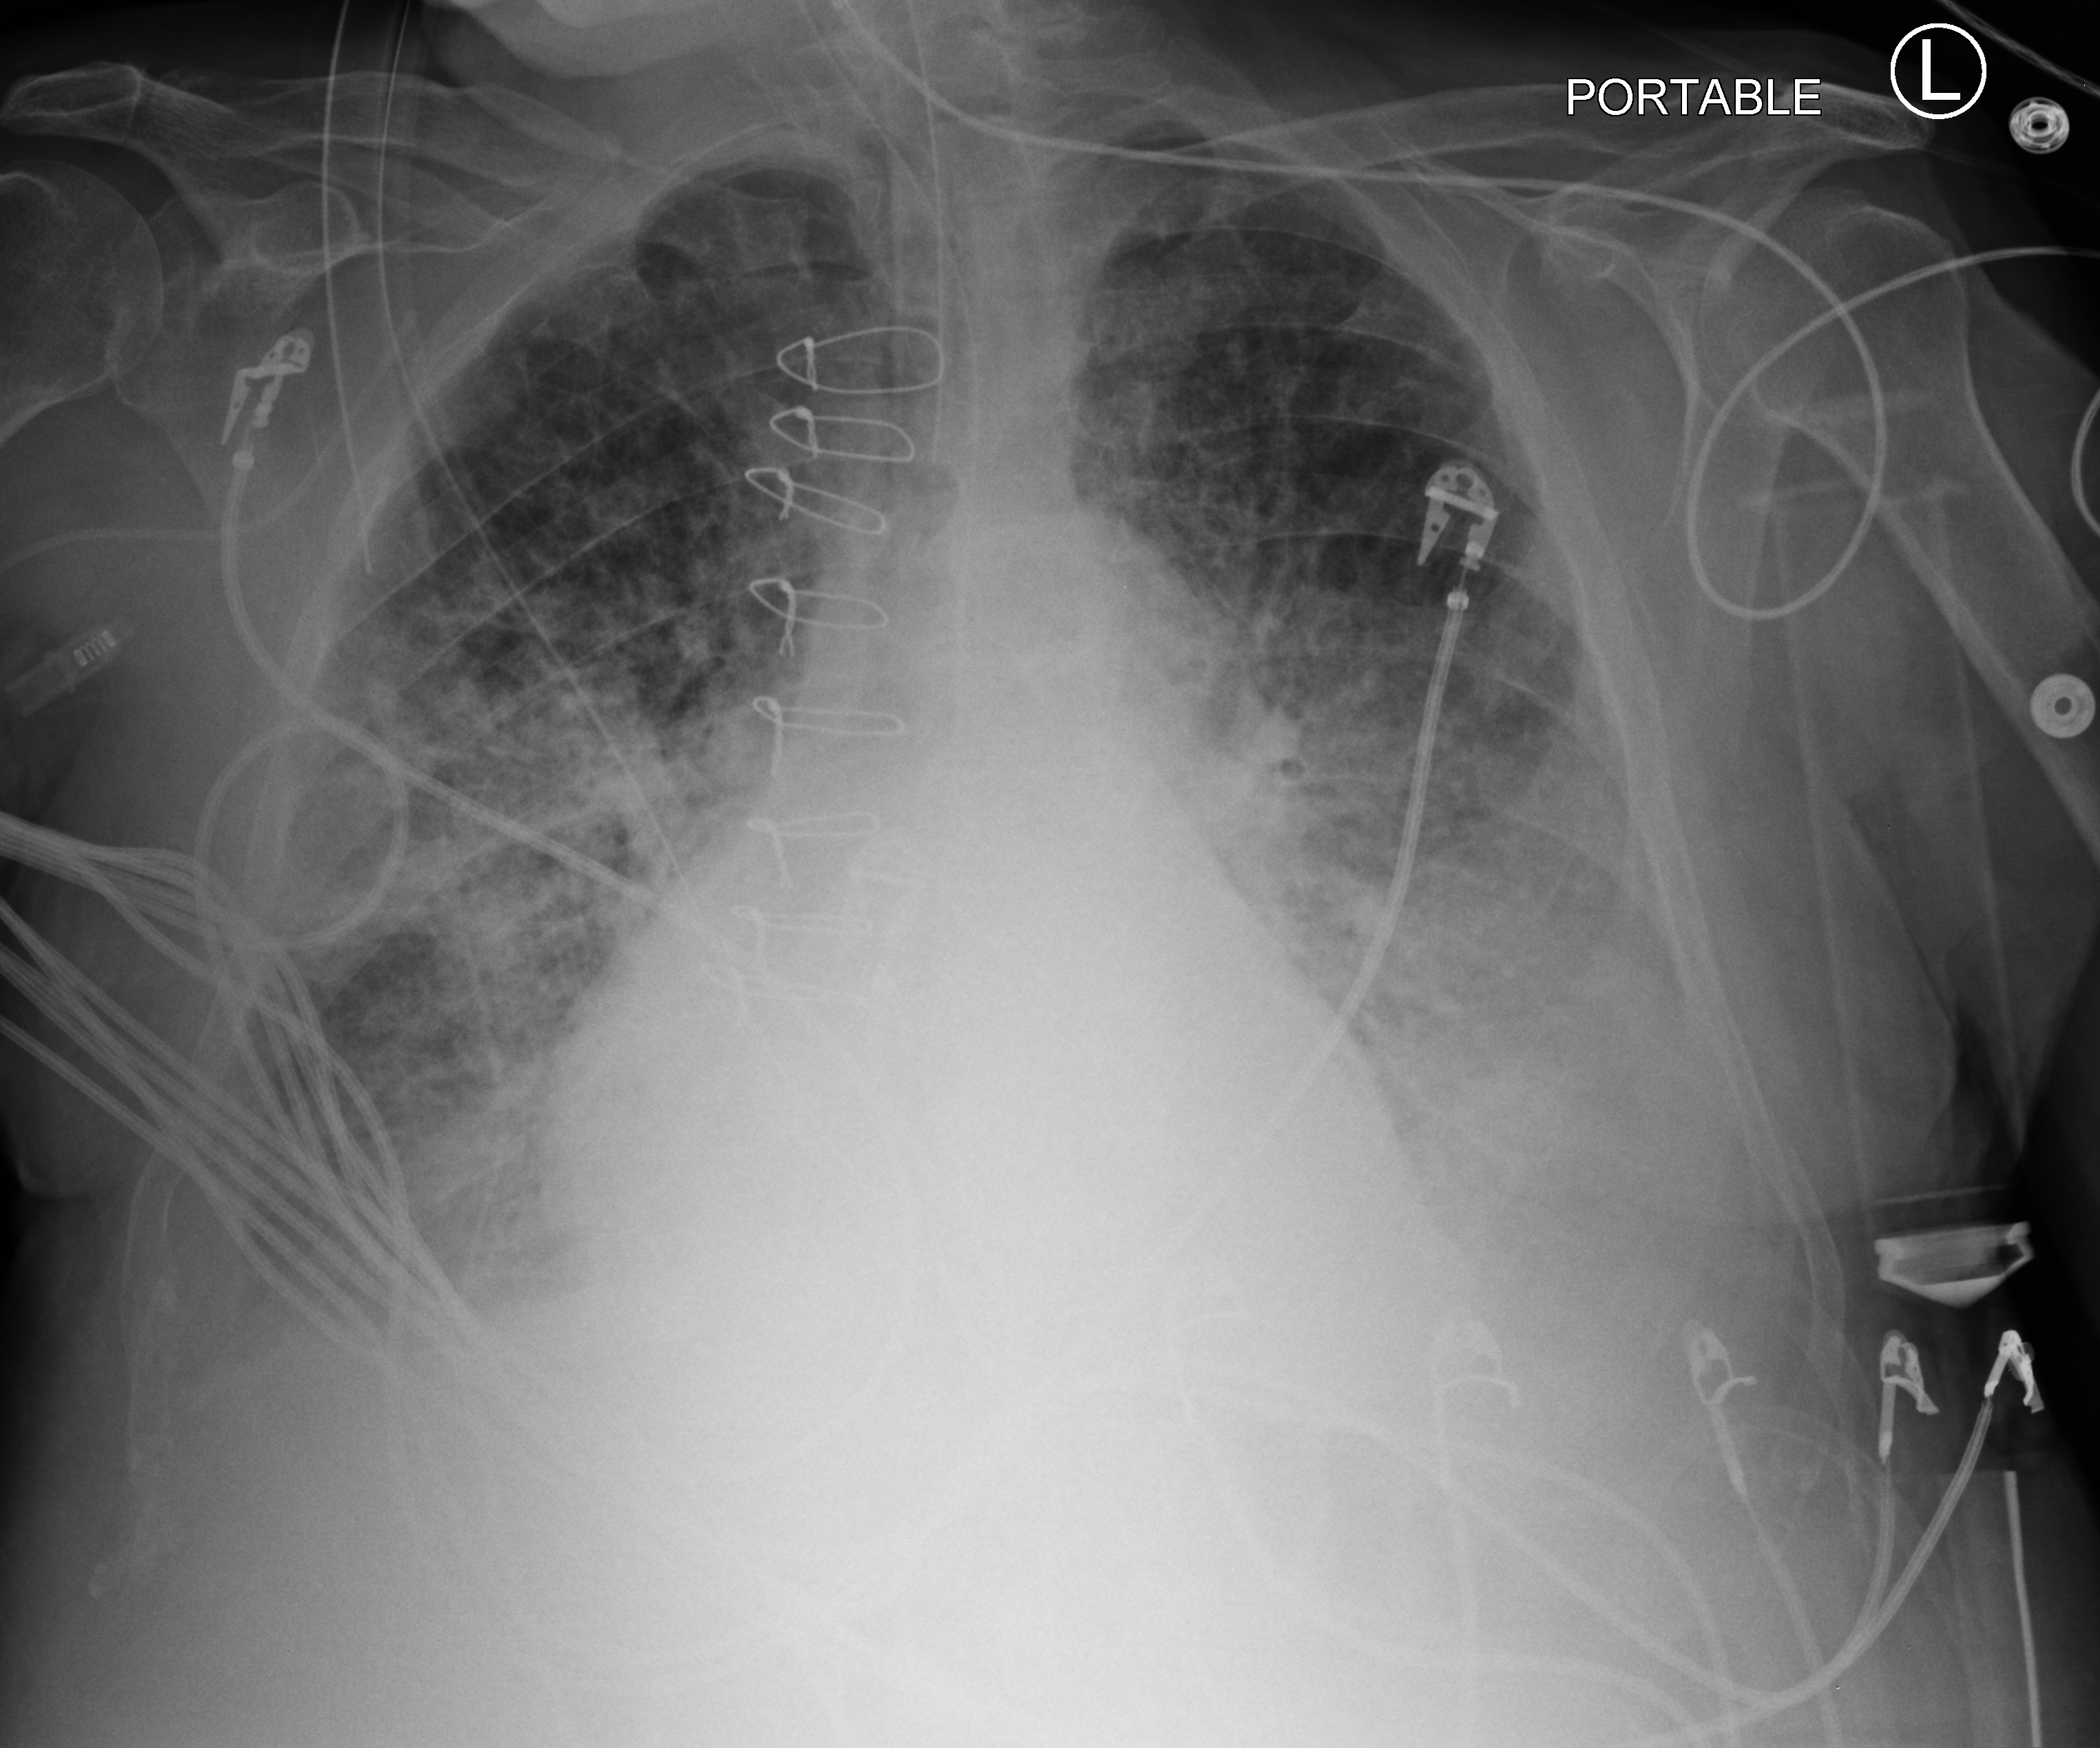
Portable chest radiograph; anteroposterior (AP) projection. Male patient hospitalised with COVID-19, age 75–90 years.
Admission-level facts for this patient (not findings on this image; timing relative to this image not recorded): admitted to intensive care during this hospital stay: yes; mechanically ventilated during this hospital stay: yes.